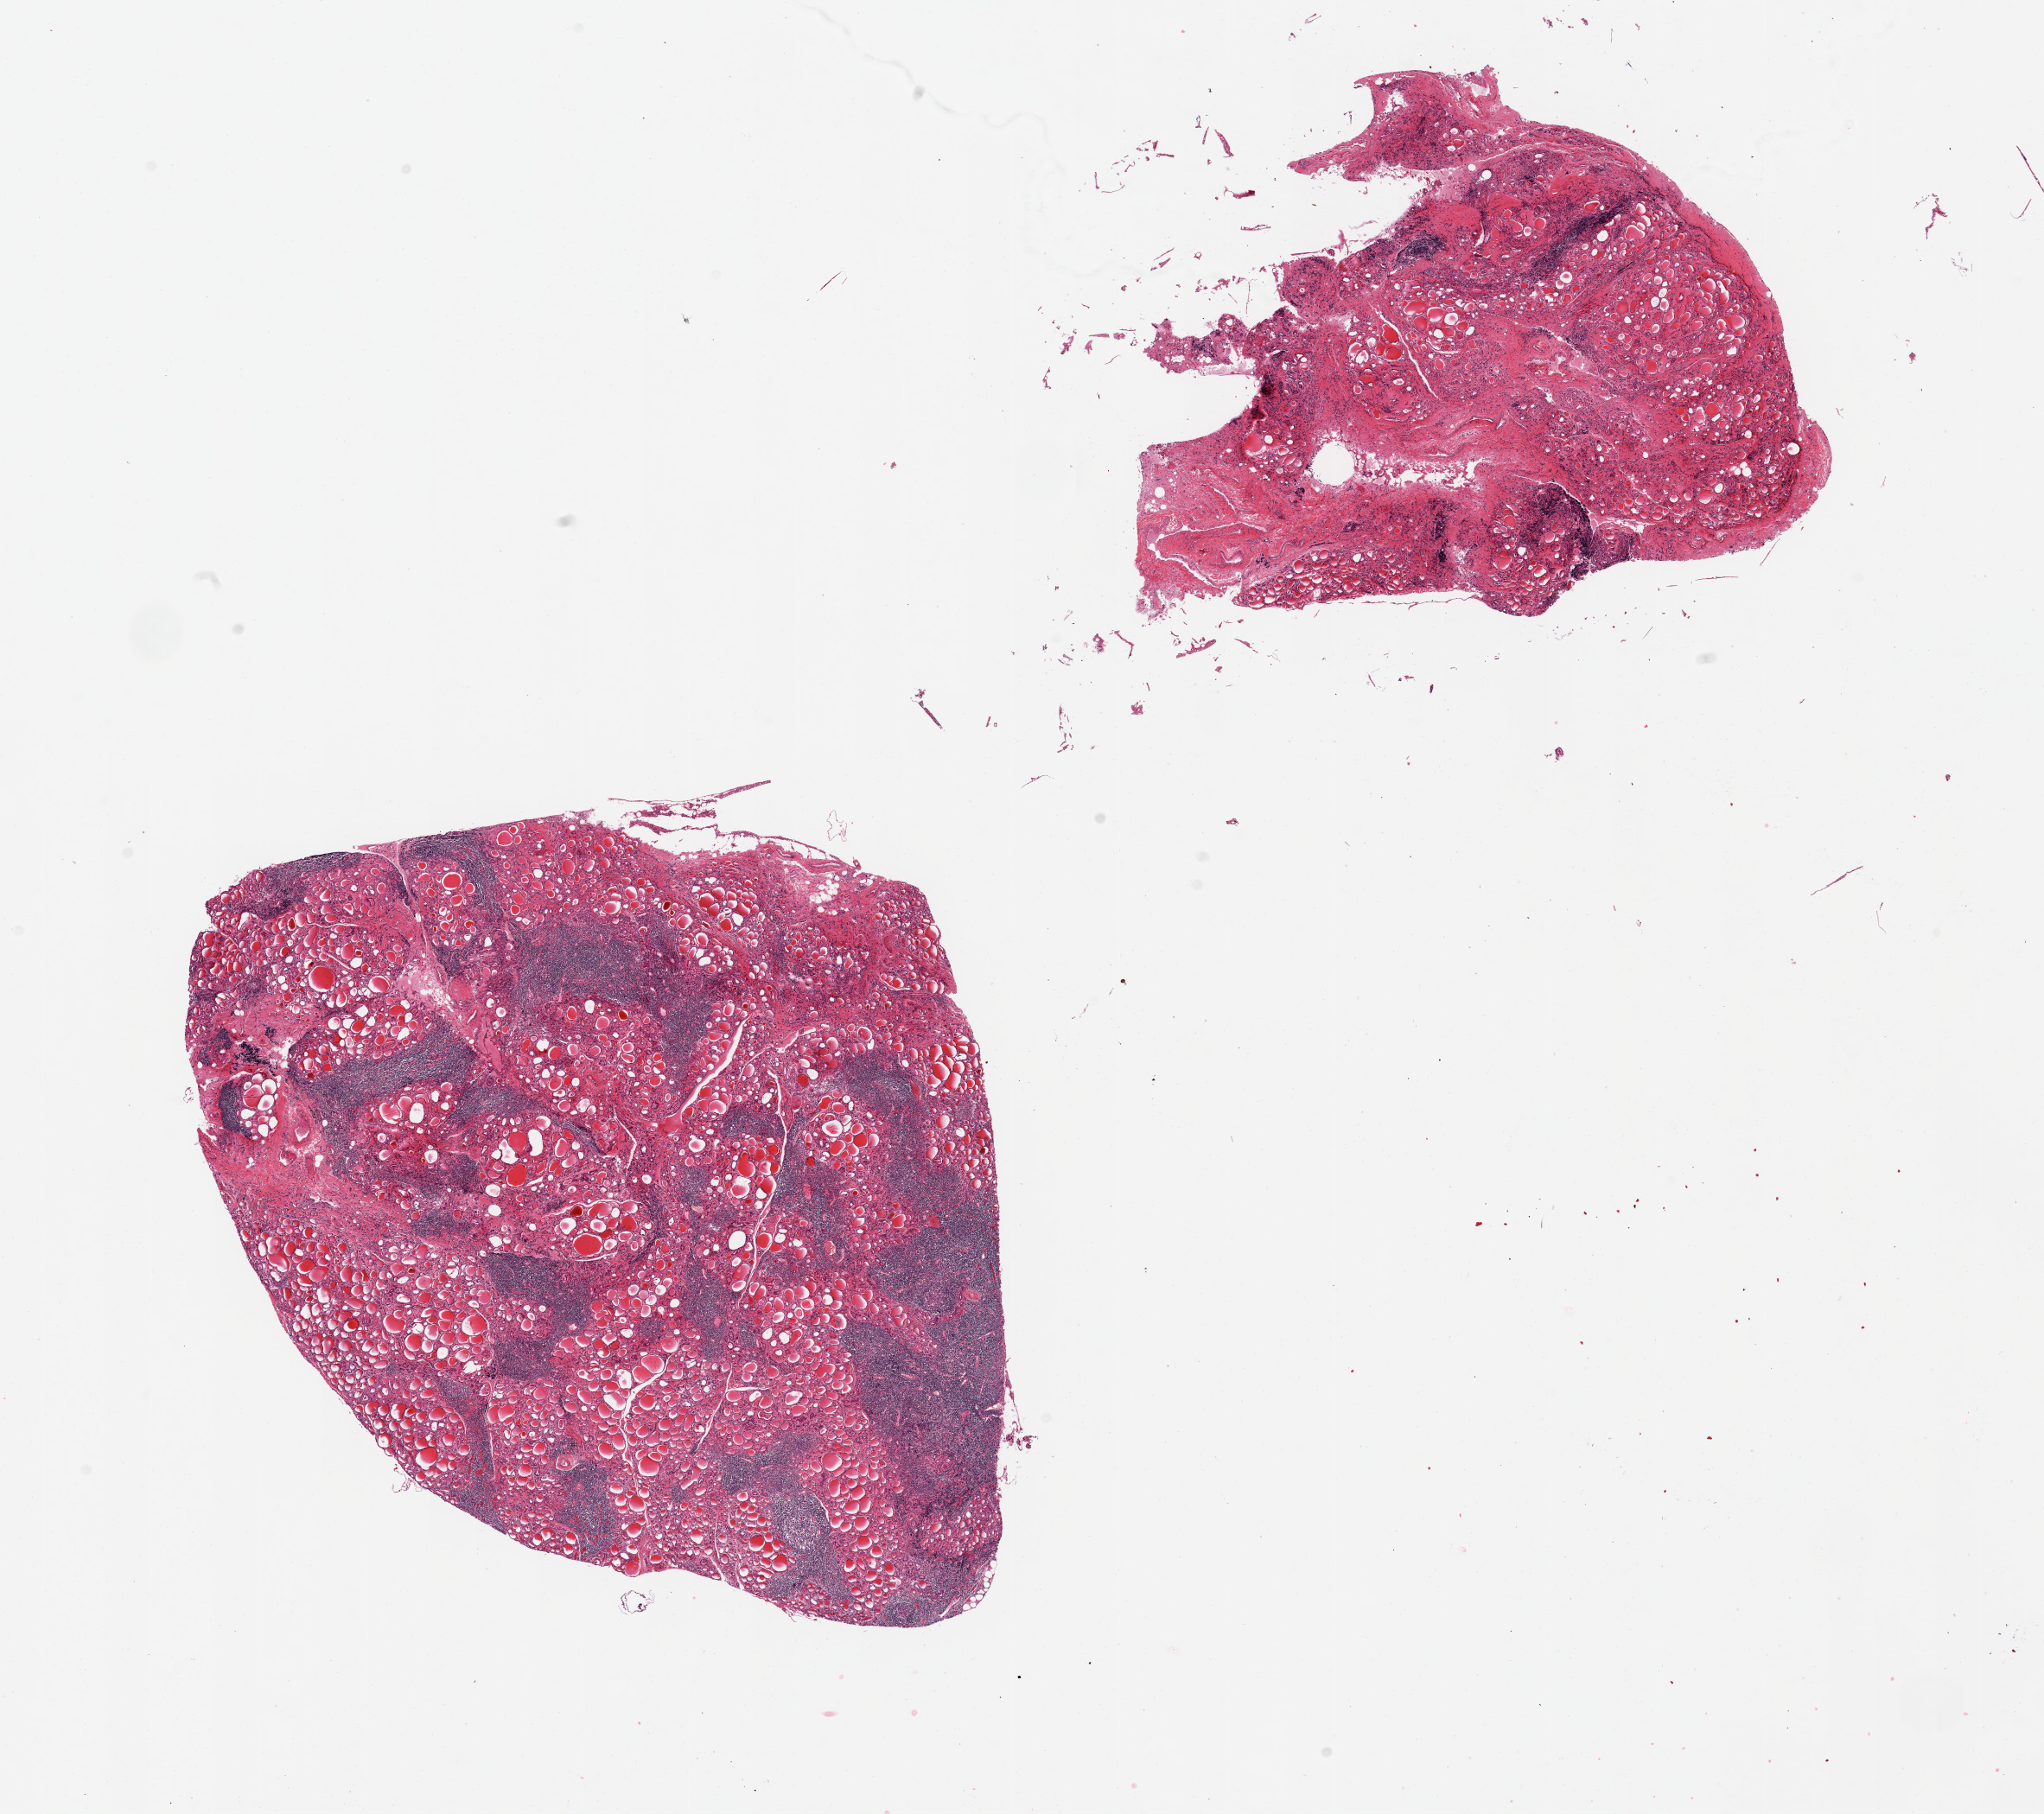
Hematoxylin and eosin (H&E) whole-slide image, a low-resolution overview of the entire scanned area, about 18.7 x 16.6 mm (from a 20x scan); PAXgene-fixed, paraffin-embedded tissue; section of thyroid (target tissue); donor tissue sample. Female donor.
• review note (as recorded): 2 pieces; moderate degree of lymphocytic (Hashimoto) thyroiditis; second piece has more fibrosis than larger piece